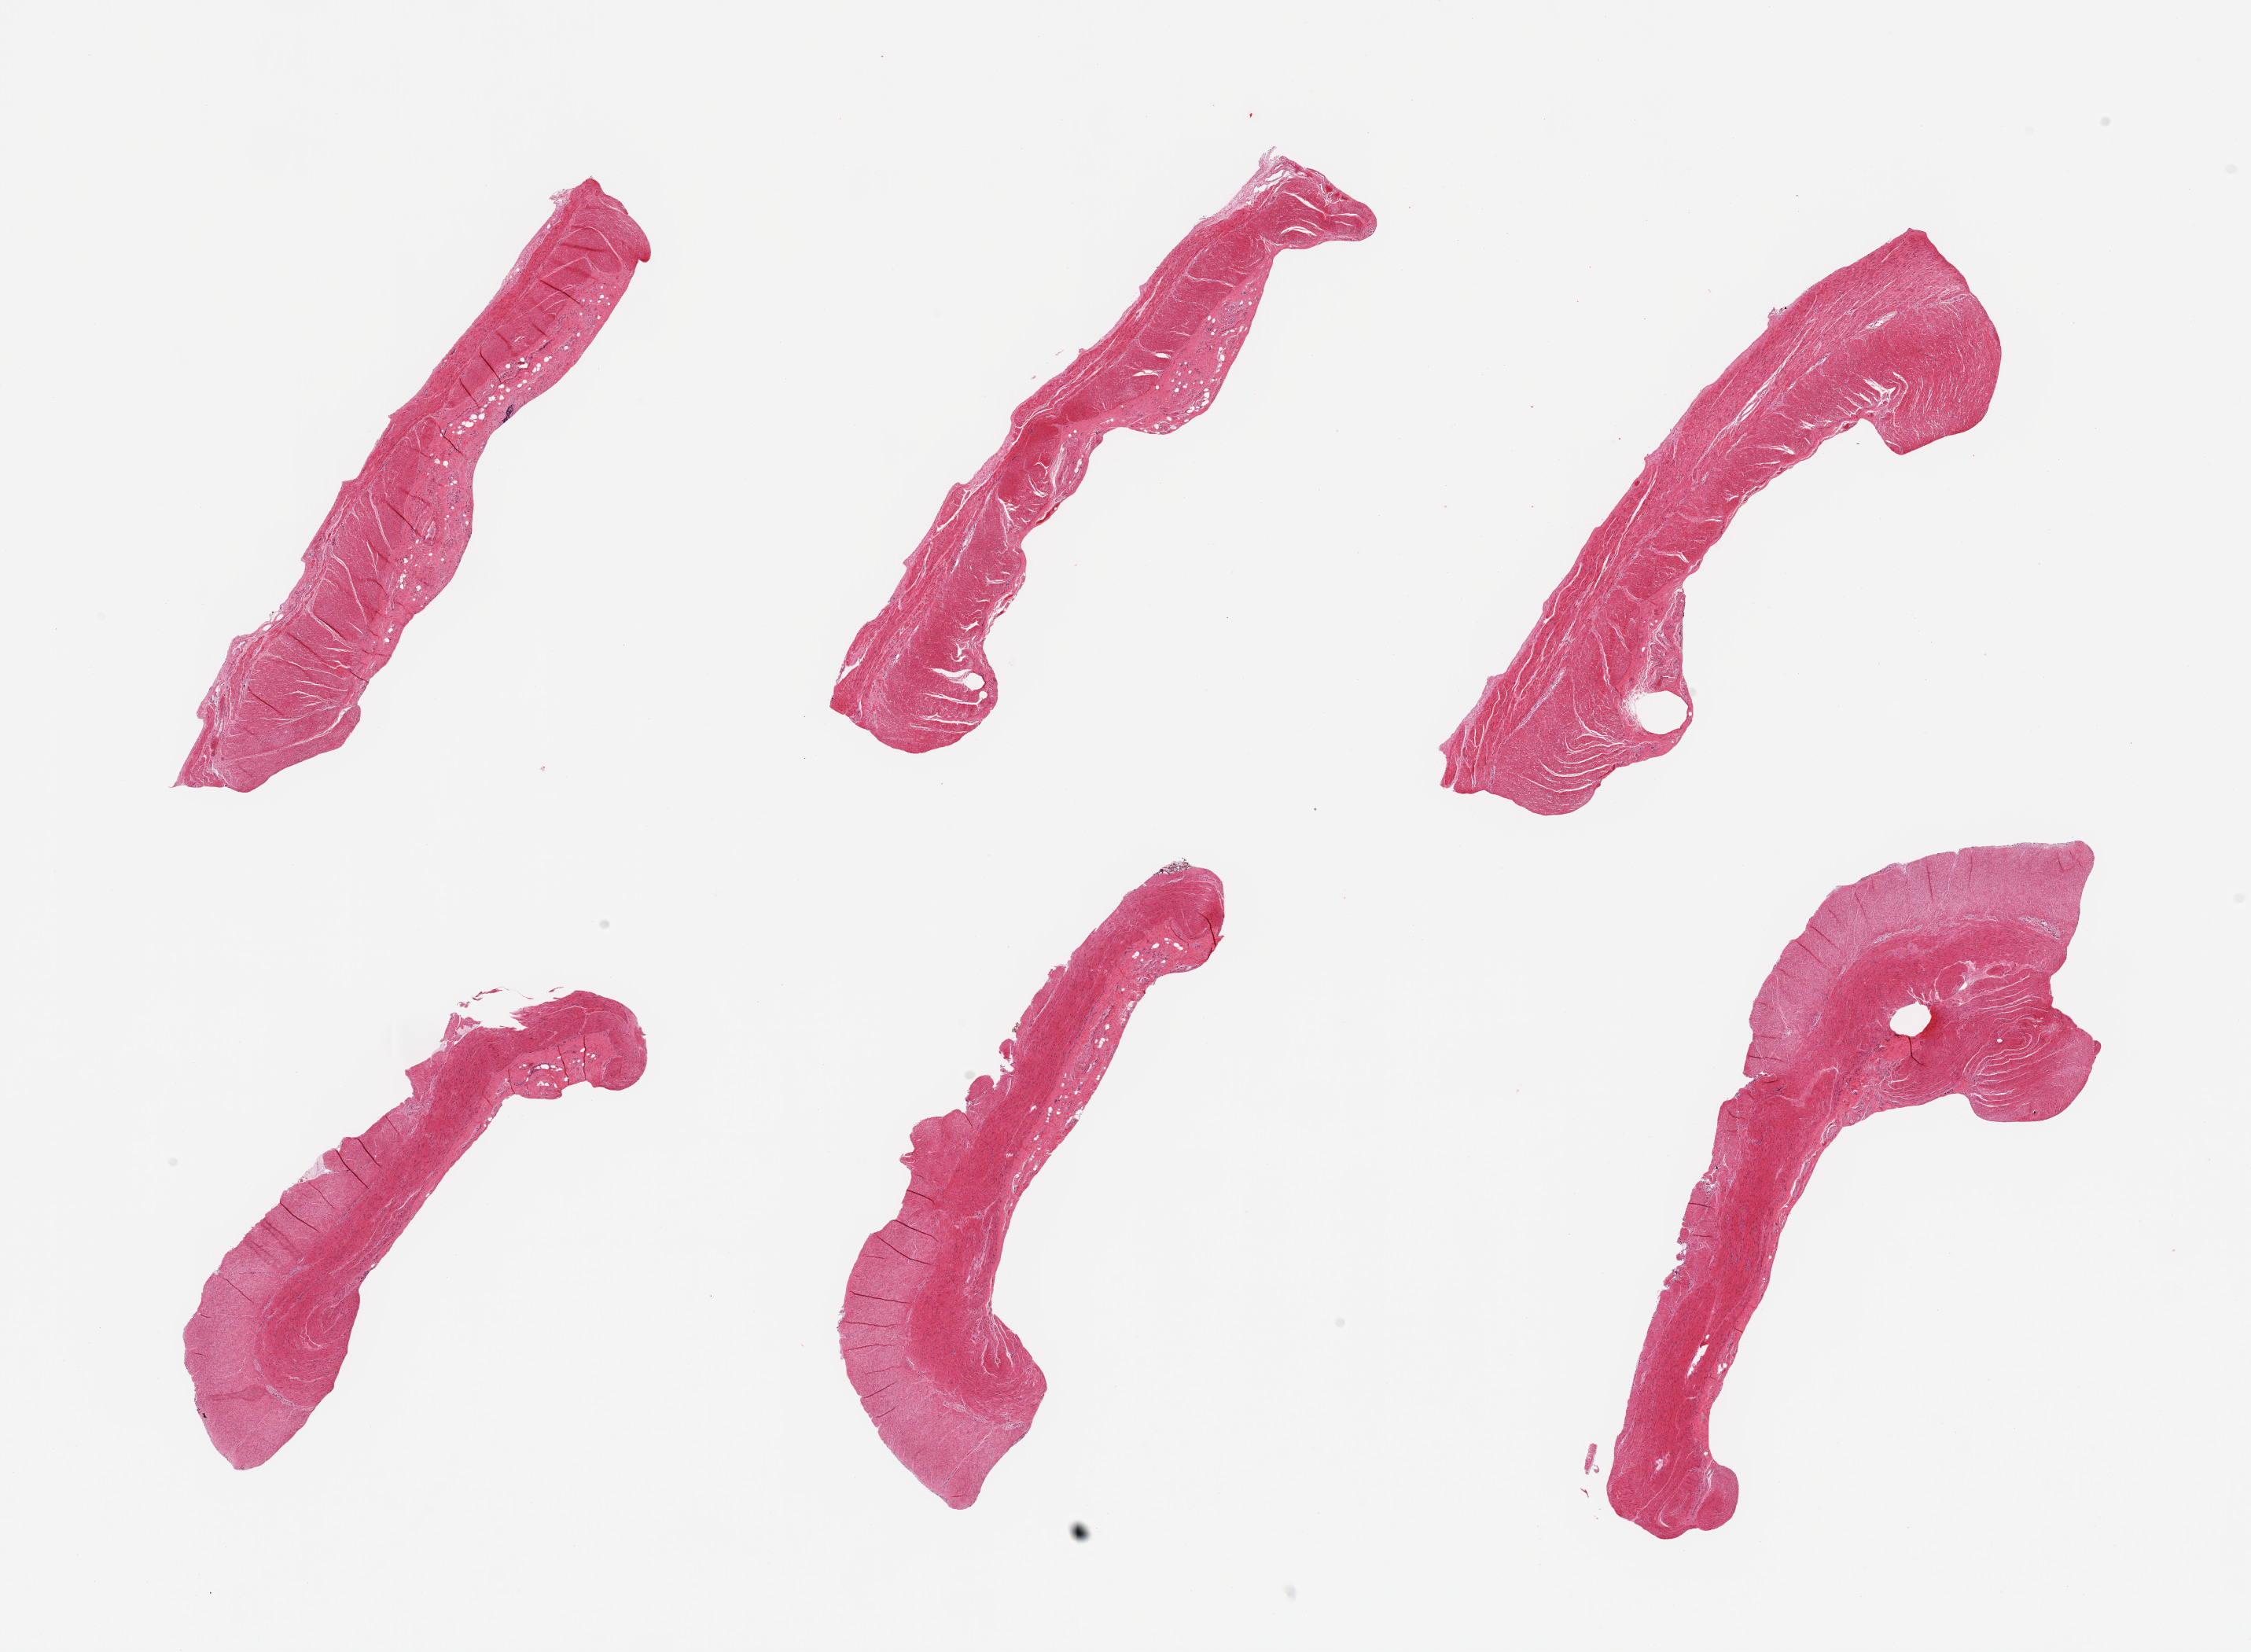
Haematoxylin and eosin whole-slide image — whole scanned area (about 22.6 x 16.6 mm) shown as a low-resolution overview. PAXgene-fixed, paraffin-embedded tissue. Target tissue: sigmoid colon. Donor tissue sample. Donor sex: female.
* review note (as recorded): 6 pieces, confirmed target muscularis